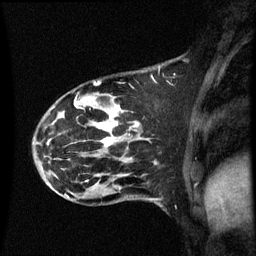
Breast MRI (dynamic contrast-enhanced), one sagittal slice. Dynamic contrast-enhanced series, image 2 of 3 at this slice position (ordered by acquisition). 1.5 T. TE 4.2 ms, TR 8.9 ms. 2 mm slice thickness. 256 × 256 image matrix. Female patient, age 44 years. Case-level facts recorded for this patient, not image findings: setting: breast cancer imaged before/during neoadjuvant chemotherapy; receptor status: HR-positive, HER2-negative.
Outlined on this slice (semi-automatic segmentation, software-assisted and operator-edited):
- analysis volume of interest (the breast-tissue region the enhancement analysis was run in; not a lesion): box from (x=43, y=88) to (x=151, y=189) px
- tumour enhancement mask (voxels above the 70 % enhancement threshold inside the analysis volume of interest): (x=76, y=106)–(x=139, y=145)